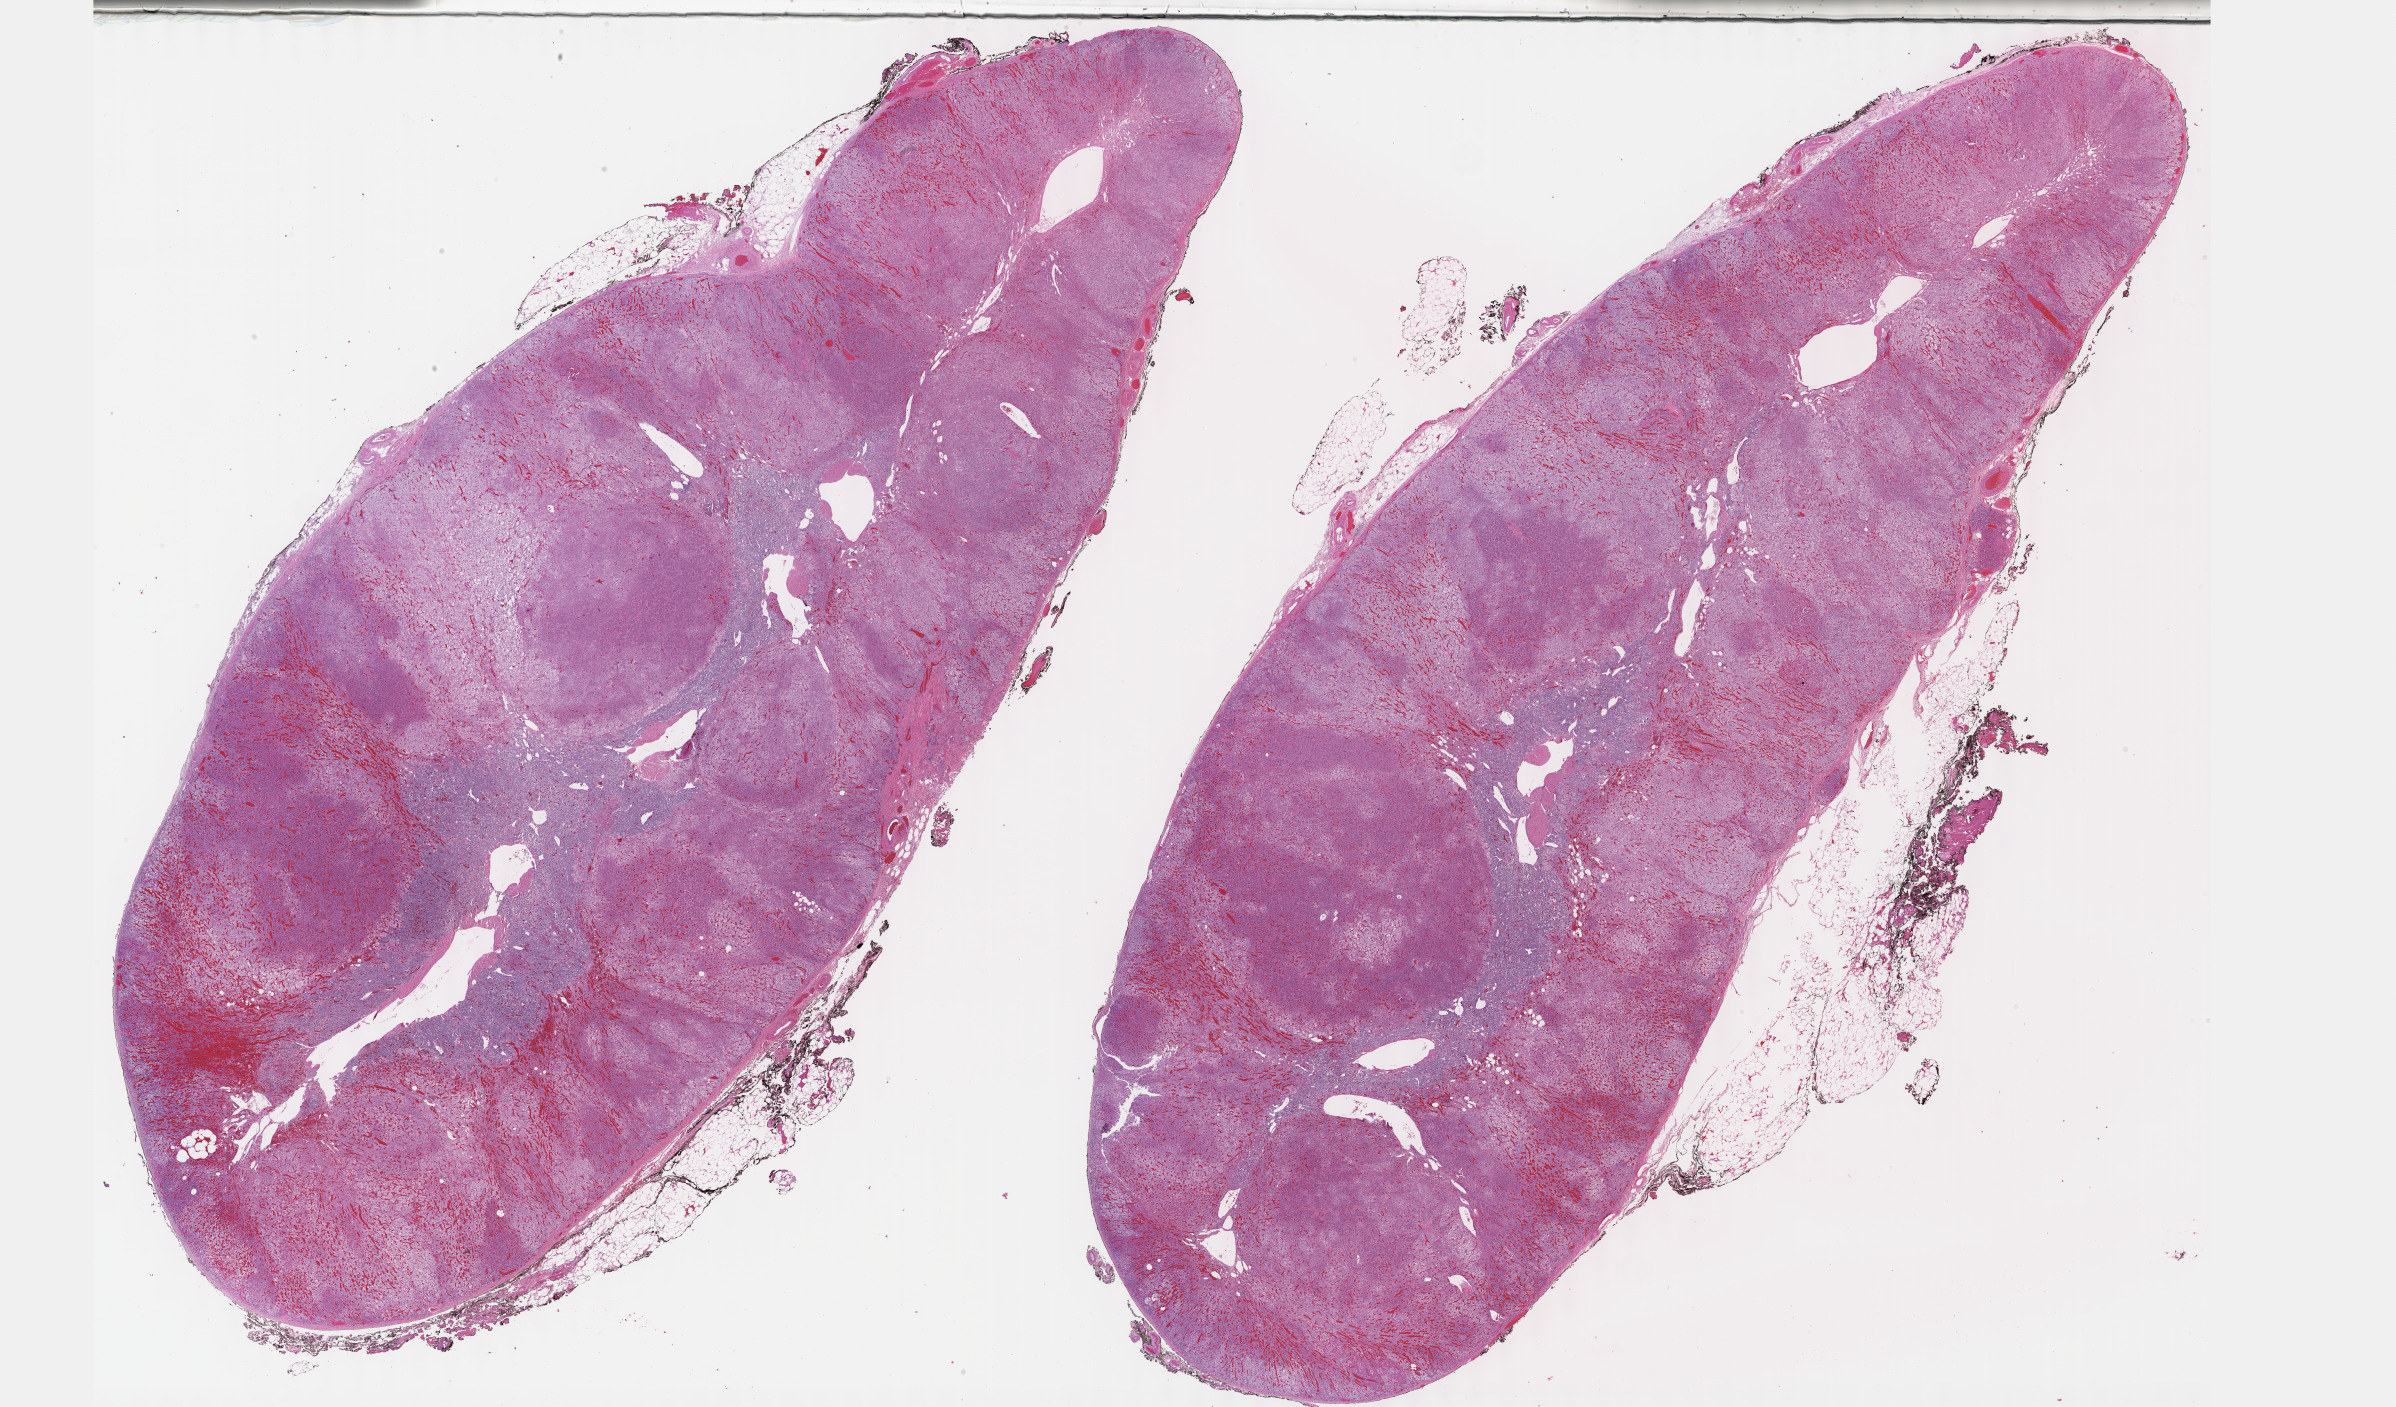
Whole-slide histology image, H&E, whole scanned area (about 38.7 x 22.7 mm) shown as a low-resolution overview, FFPE section, adrenal gland, primary tumour sample. Male patient; age at initial diagnosis 54 years.
Diagnosis: Pheochromocytoma, NOS.